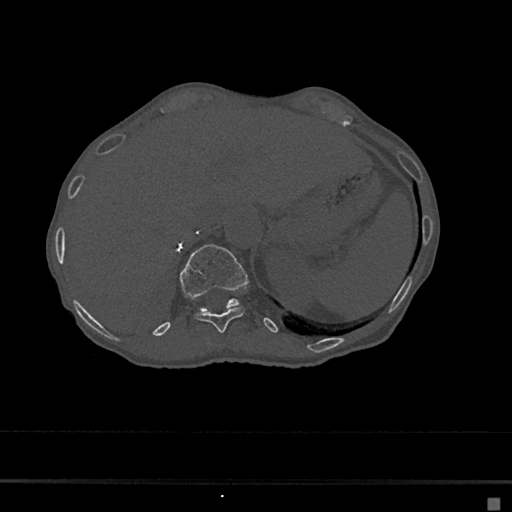
CT including the spine, one axial slice. Position 155 of 797 along the scan axis. Reconstruction kernel Br40s/3. 120 kVp. Bone window (W 1800 / L 400 HU). 512 × 512 image matrix, field of view 360 × 360 mm. Female patient, age 68 years. From the clinical record (not read from this slice): primary cancer: renal.
Structures marked on this image (semi-automatic segmentation, software-assisted and operator-edited):
- T11 vertebra: bounding box (x1, y1, x2, y2) in pixels: (195, 307, 244, 333)
- T12 vertebra: (179, 244, 248, 311)